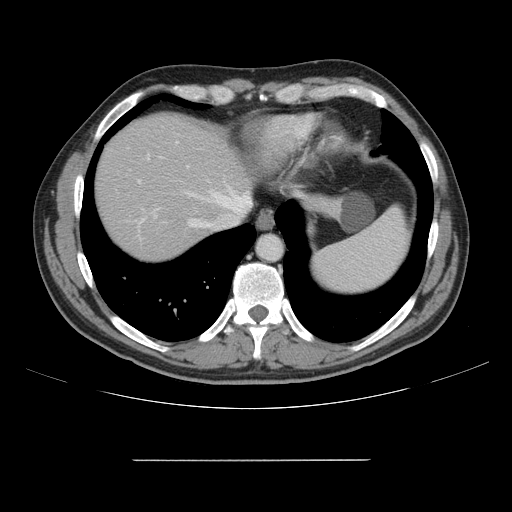
Contrast-enhanced abdominal CT, one axial slice. Position 134 of 164 along the scan axis. Intravenous contrast given. Soft-tissue window (W 400 / L 40 HU). 2.5 mm slice thickness. 512 × 512 image matrix, field of view 404 × 404 mm. Male patient, age 54 years. Case-level facts recorded for this patient, not image findings: diagnosis: colorectal cancer liver metastases, imaged before liver resection; multiple liver metastases: yes; largest metastasis: 1 cm; disease in both lobes: no.
Annotated regions visible in this slice (outlined manually by an expert reader):
- hepatic veins: bounding box [x1, y1, x2, y2] px = [185, 190, 251, 227]
- liver: [96, 116, 324, 261]
- planned liver remnant (the part of the liver to remain after resection): [96, 116, 247, 261]
- portal vein (with intrahepatic branches): [138, 142, 178, 220]